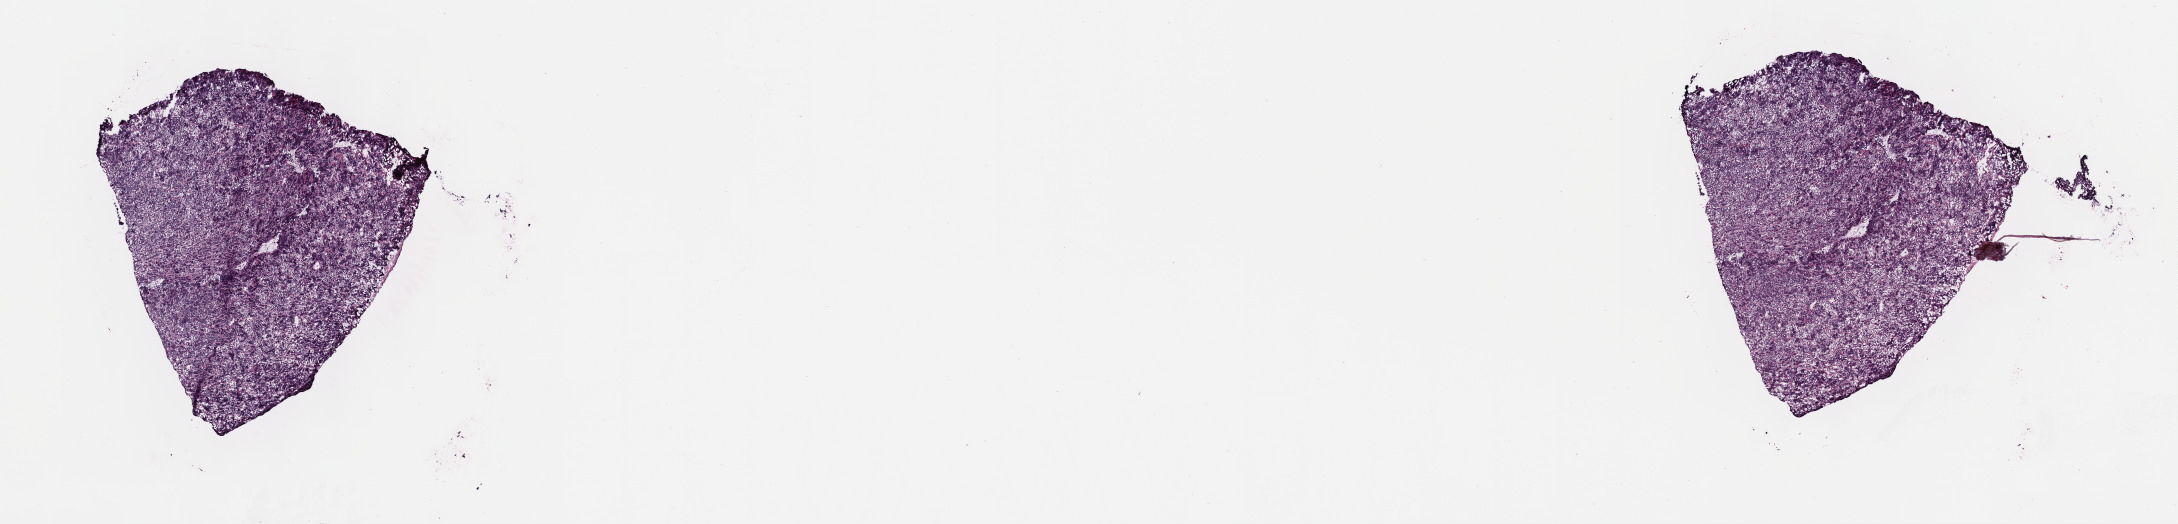
Whole-slide image, H&E stain, whole scanned area (about 17.6 x 4.2 mm) shown as a low-resolution overview. Frozen section. Primary tumor. Site: mouth. Patient: female, age at initial diagnosis 7 years. Pathologist review of this section (percent, as recorded): tumor cells 90%, tumor nuclei 95%, stromal cells 5%, necrosis 0%, normal cells 5%. Inflammatory infiltration, as recorded: lymphocyte infiltration 50%, monocyte infiltration 40%, neutrophil infiltration 0%.
• section: bottom of the tissue portion
• histologic diagnosis: Diffuse large B-cell lymphoma, NOS
• Ann Arbor stage (patient): Stage III